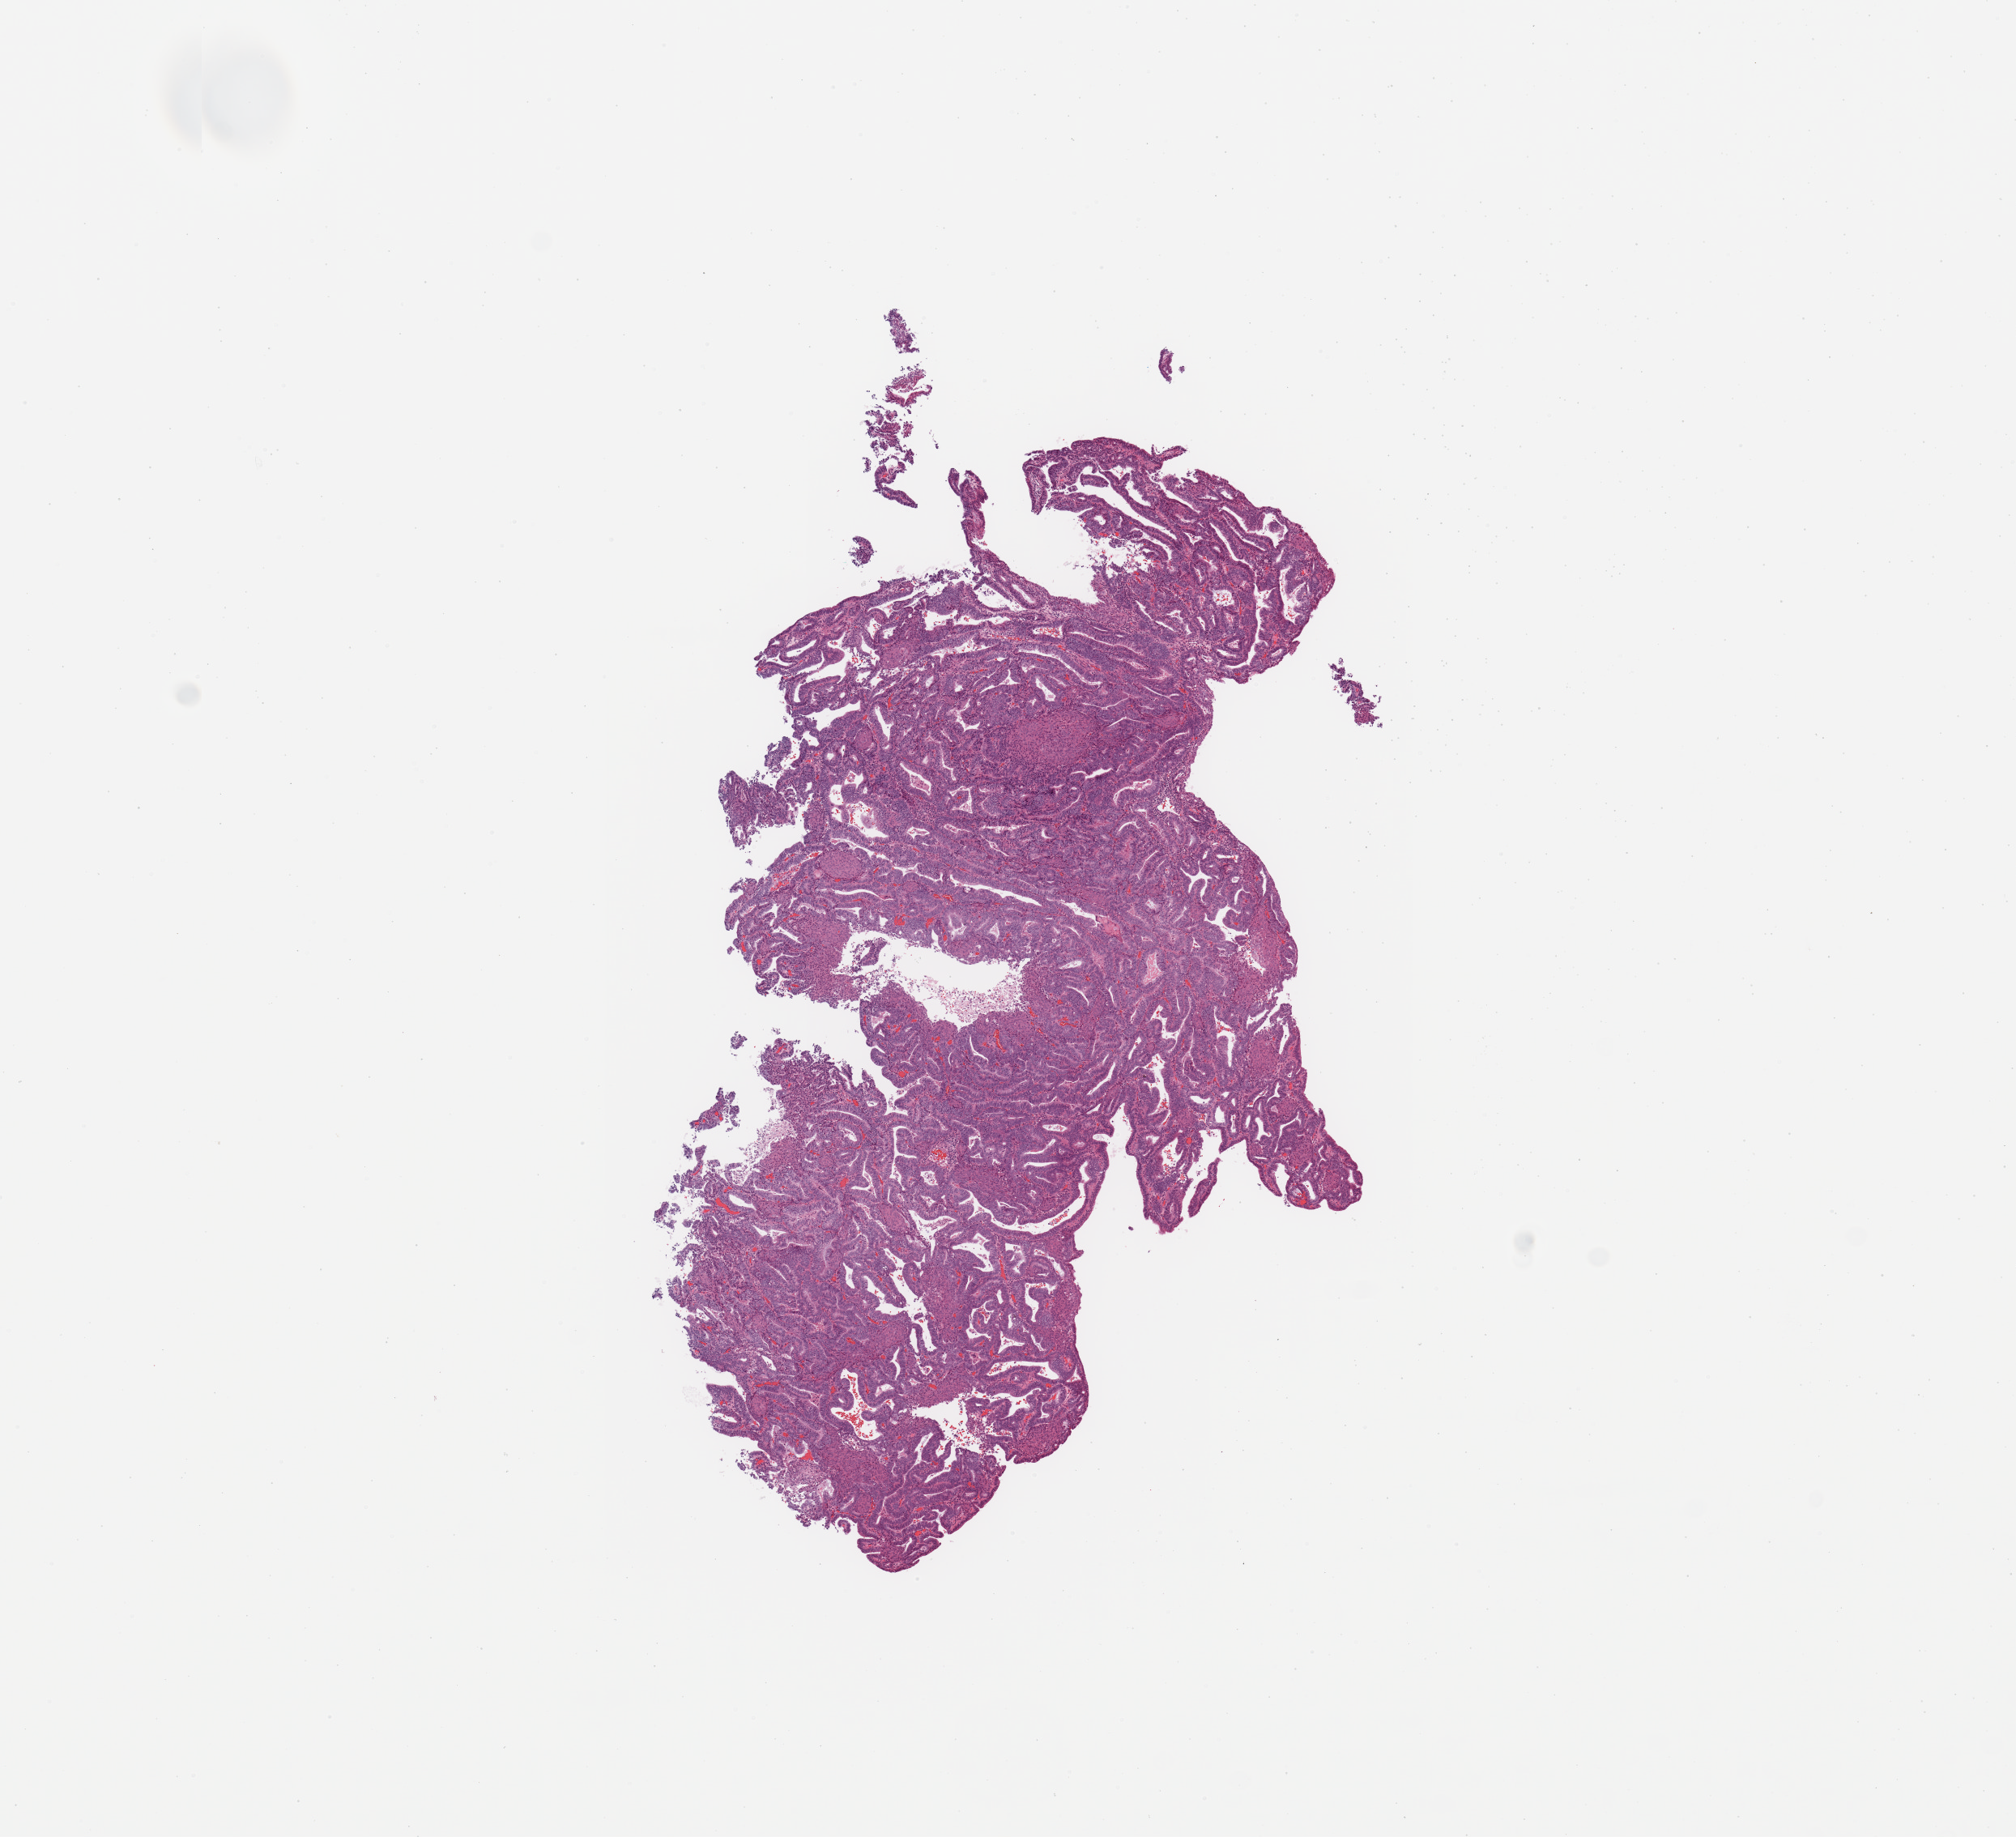
Whole-slide histology image, H&E, low-resolution overview of the scanned area, about 9.8 x 9.0 mm (slide scanned at 20x), uterus, tumour tissue. Female, 56 y/o. Histologic grade: G1 (well differentiated).
AJCC pathologic stage: I. Histologic diagnosis: Endometrioid adenocarcinoma, NOS.